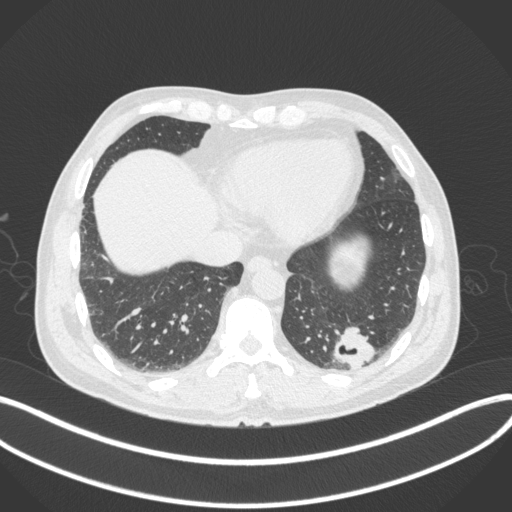
Chest CT, one axial slice. Position 69 of 313 along the scan axis. Reconstruction kernel B31f. Lung window (W 1500 / L -600 HU). 512 × 512 image matrix, field of view 400 × 400 mm. Male patient, age 54 years. From the clinical record (not read from this slice): clinical TNM (as recorded): T1c N0 M1.
Annotated regions visible in this slice (rectangle marked by the reading radiologist):
- lung tumour (recorded histology: adenocarcinoma): box from (x=327, y=321) to (x=375, y=371) px